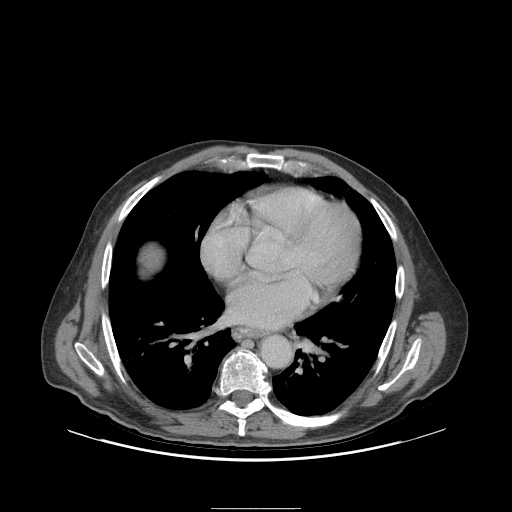
Contrast-enhanced abdominal CT (liver protocol), one axial slice. Slice 101 of 105 in the series (ordered by position). Soft-tissue window (W 400 / L 40 HU). 2.5 mm slice thickness. 512 × 512 image matrix, field of view 440 × 440 mm. Case-level facts recorded for this patient, not image findings: diagnosis: hepatocellular carcinoma (patient treated with transarterial chemoembolisation; whether this scan precedes or follows treatment is not stated here); TNM stage (as recorded): Stage-I; Child-Pugh class: A; tumour size: 5.1 cm.
Structures marked on this image (semi-automatic segmentation, software-assisted and operator-edited):
- liver parenchyma outside the tumour (the mass and vessels are separate outlines, so this box may not span the whole liver): box from (x=142, y=245) to (x=162, y=270) px